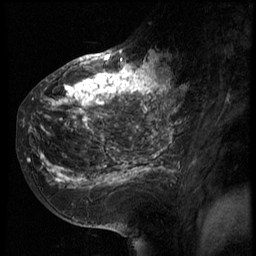
Breast MRI (dynamic contrast-enhanced), one sagittal slice; 3 images stored at this slice position (order not interpretable as contrast timing); 1.5 T; TE 4.2 ms, TR 8.9 ms; 2.5 mm slice thickness; 256 × 256 image matrix, field of view 200 × 200 mm. Patient: female, 39 years. From the clinical record (not read from this slice): setting: breast cancer imaged before/during neoadjuvant chemotherapy; receptor status: HER2-positive.
Structures marked on this image (semi-automatically segmented with operator editing):
- analysis volume of interest (the breast-tissue region the enhancement analysis was run in; not a lesion): bounding box (x1, y1, x2, y2) in pixels: (29, 44, 166, 196)
- tumour enhancement mask (voxels above the 140 % enhancement threshold inside the analysis volume of interest): (29, 55, 166, 187)